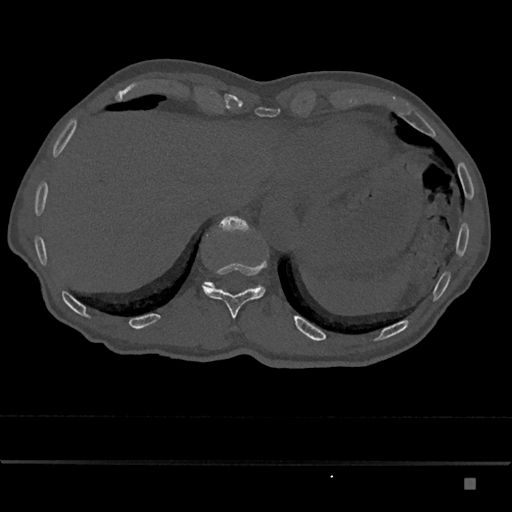
CT including the spine, one axial slice; position 665 of 797 along the scan axis; 120 kVp; bone window (W 1800 / L 400 HU); 0.5 mm slice thickness; 512 × 512 image matrix, field of view 390 × 390 mm. Patient: male, 72 years. From the clinical record (not read from this slice): primary cancer: prostate.
Structures marked on this image (semi-automatically segmented with operator editing):
- T11 vertebra: bounding box [x1, y1, x2, y2] px = [202, 261, 267, 319]
- T12 vertebra: [204, 216, 262, 288]